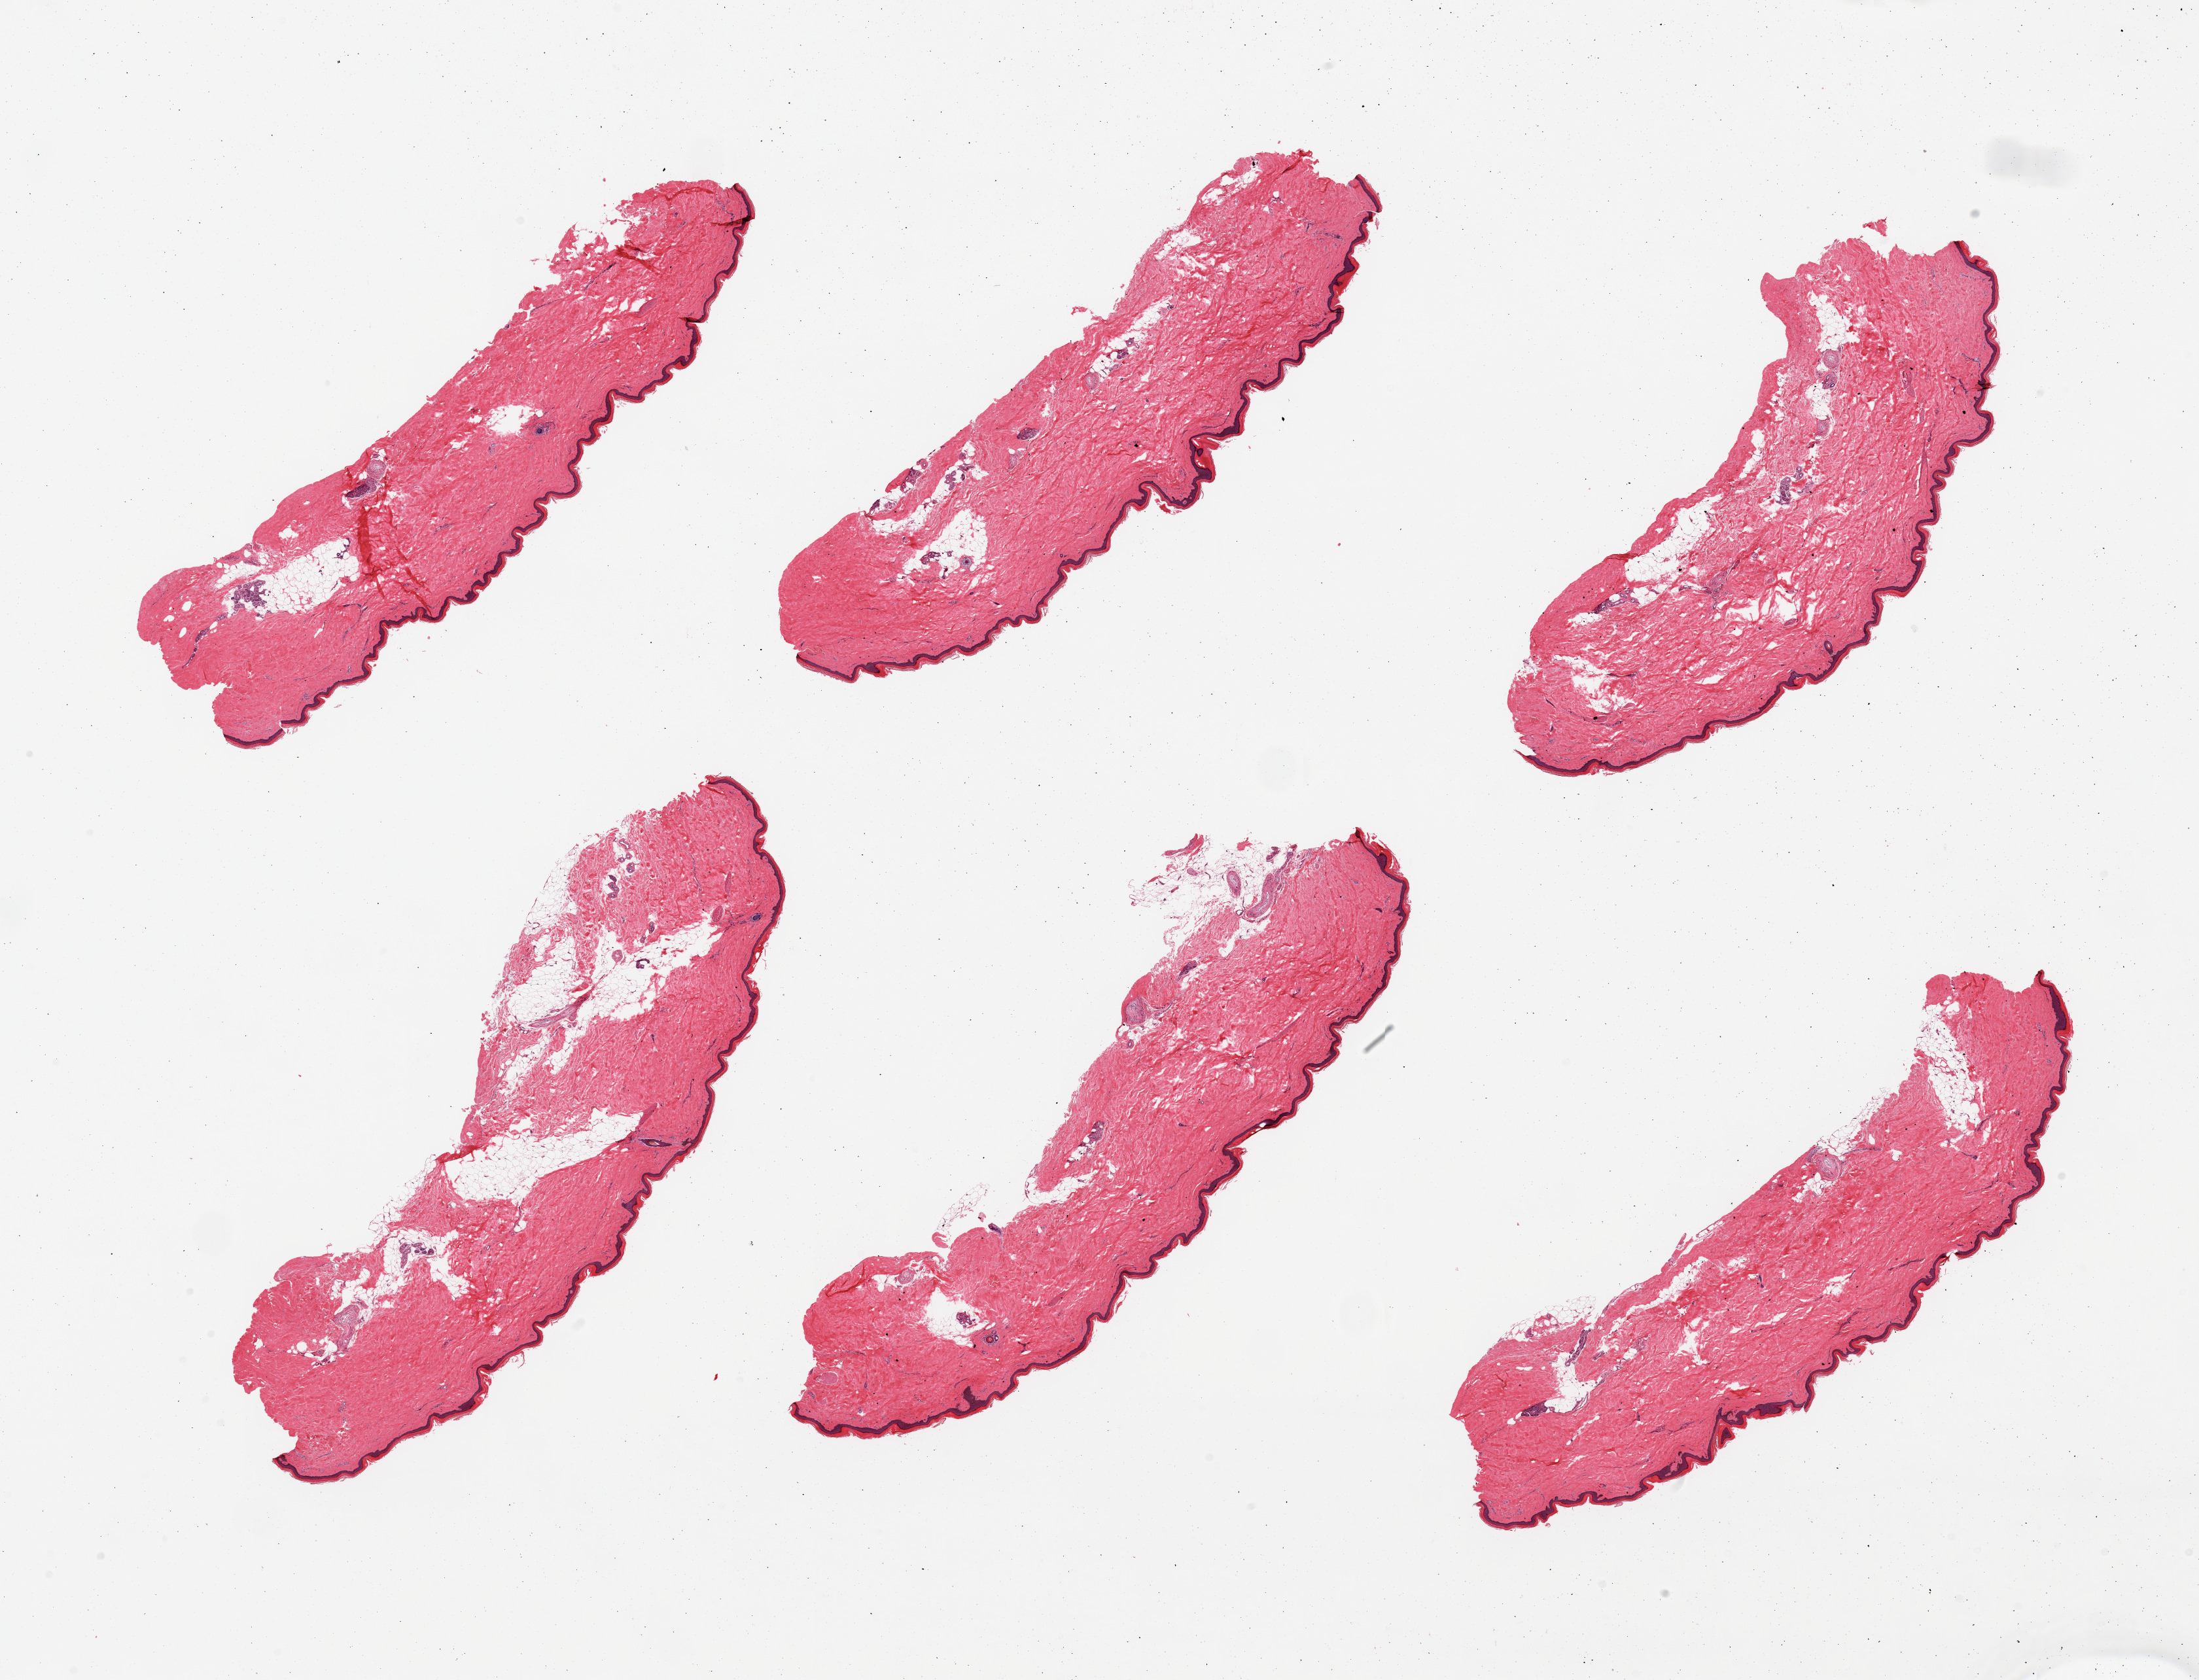
Digitized hematoxylin and eosin (H&E)-stained section — a low-resolution overview of the entire scanned area, about 26.6 x 20.3 mm (acquisition: 20x scan); PAXgene-fixed, paraffin-embedded tissue; section of skin of lower leg (target tissue); tissue donor sample. Donor sex: female.
• review note (as recorded): 6 pieces, minimal/negative dermal fat; squamous epithelium is ~70 microns